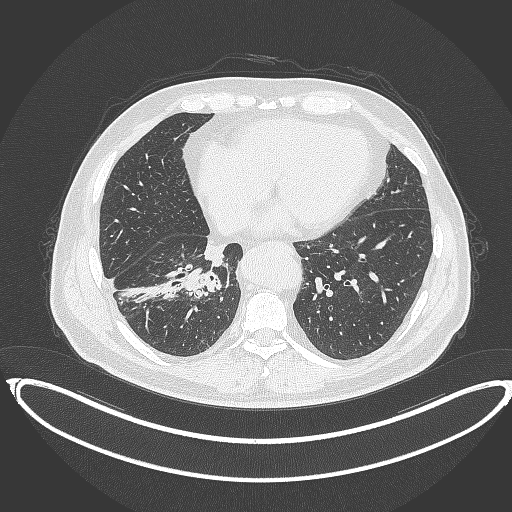
Chest CT, one axial slice; slice 145 of 387 in the series (ordered by position); reconstruction kernel B70f; 120 kVp; lung window (W 1500 / L -600 HU); 1 mm slice thickness; 512 × 512 image matrix, field of view 448 × 448 mm. Male patient, age 61 years. From the clinical record (not read from this slice): clinical TNM (as recorded): T1b N1 M0.
Annotated regions visible in this slice (rectangle marked by the reading radiologist):
- lung tumour (recorded histology: squamous cell carcinoma): bounding box [x1, y1, x2, y2] px = [182, 265, 223, 301]